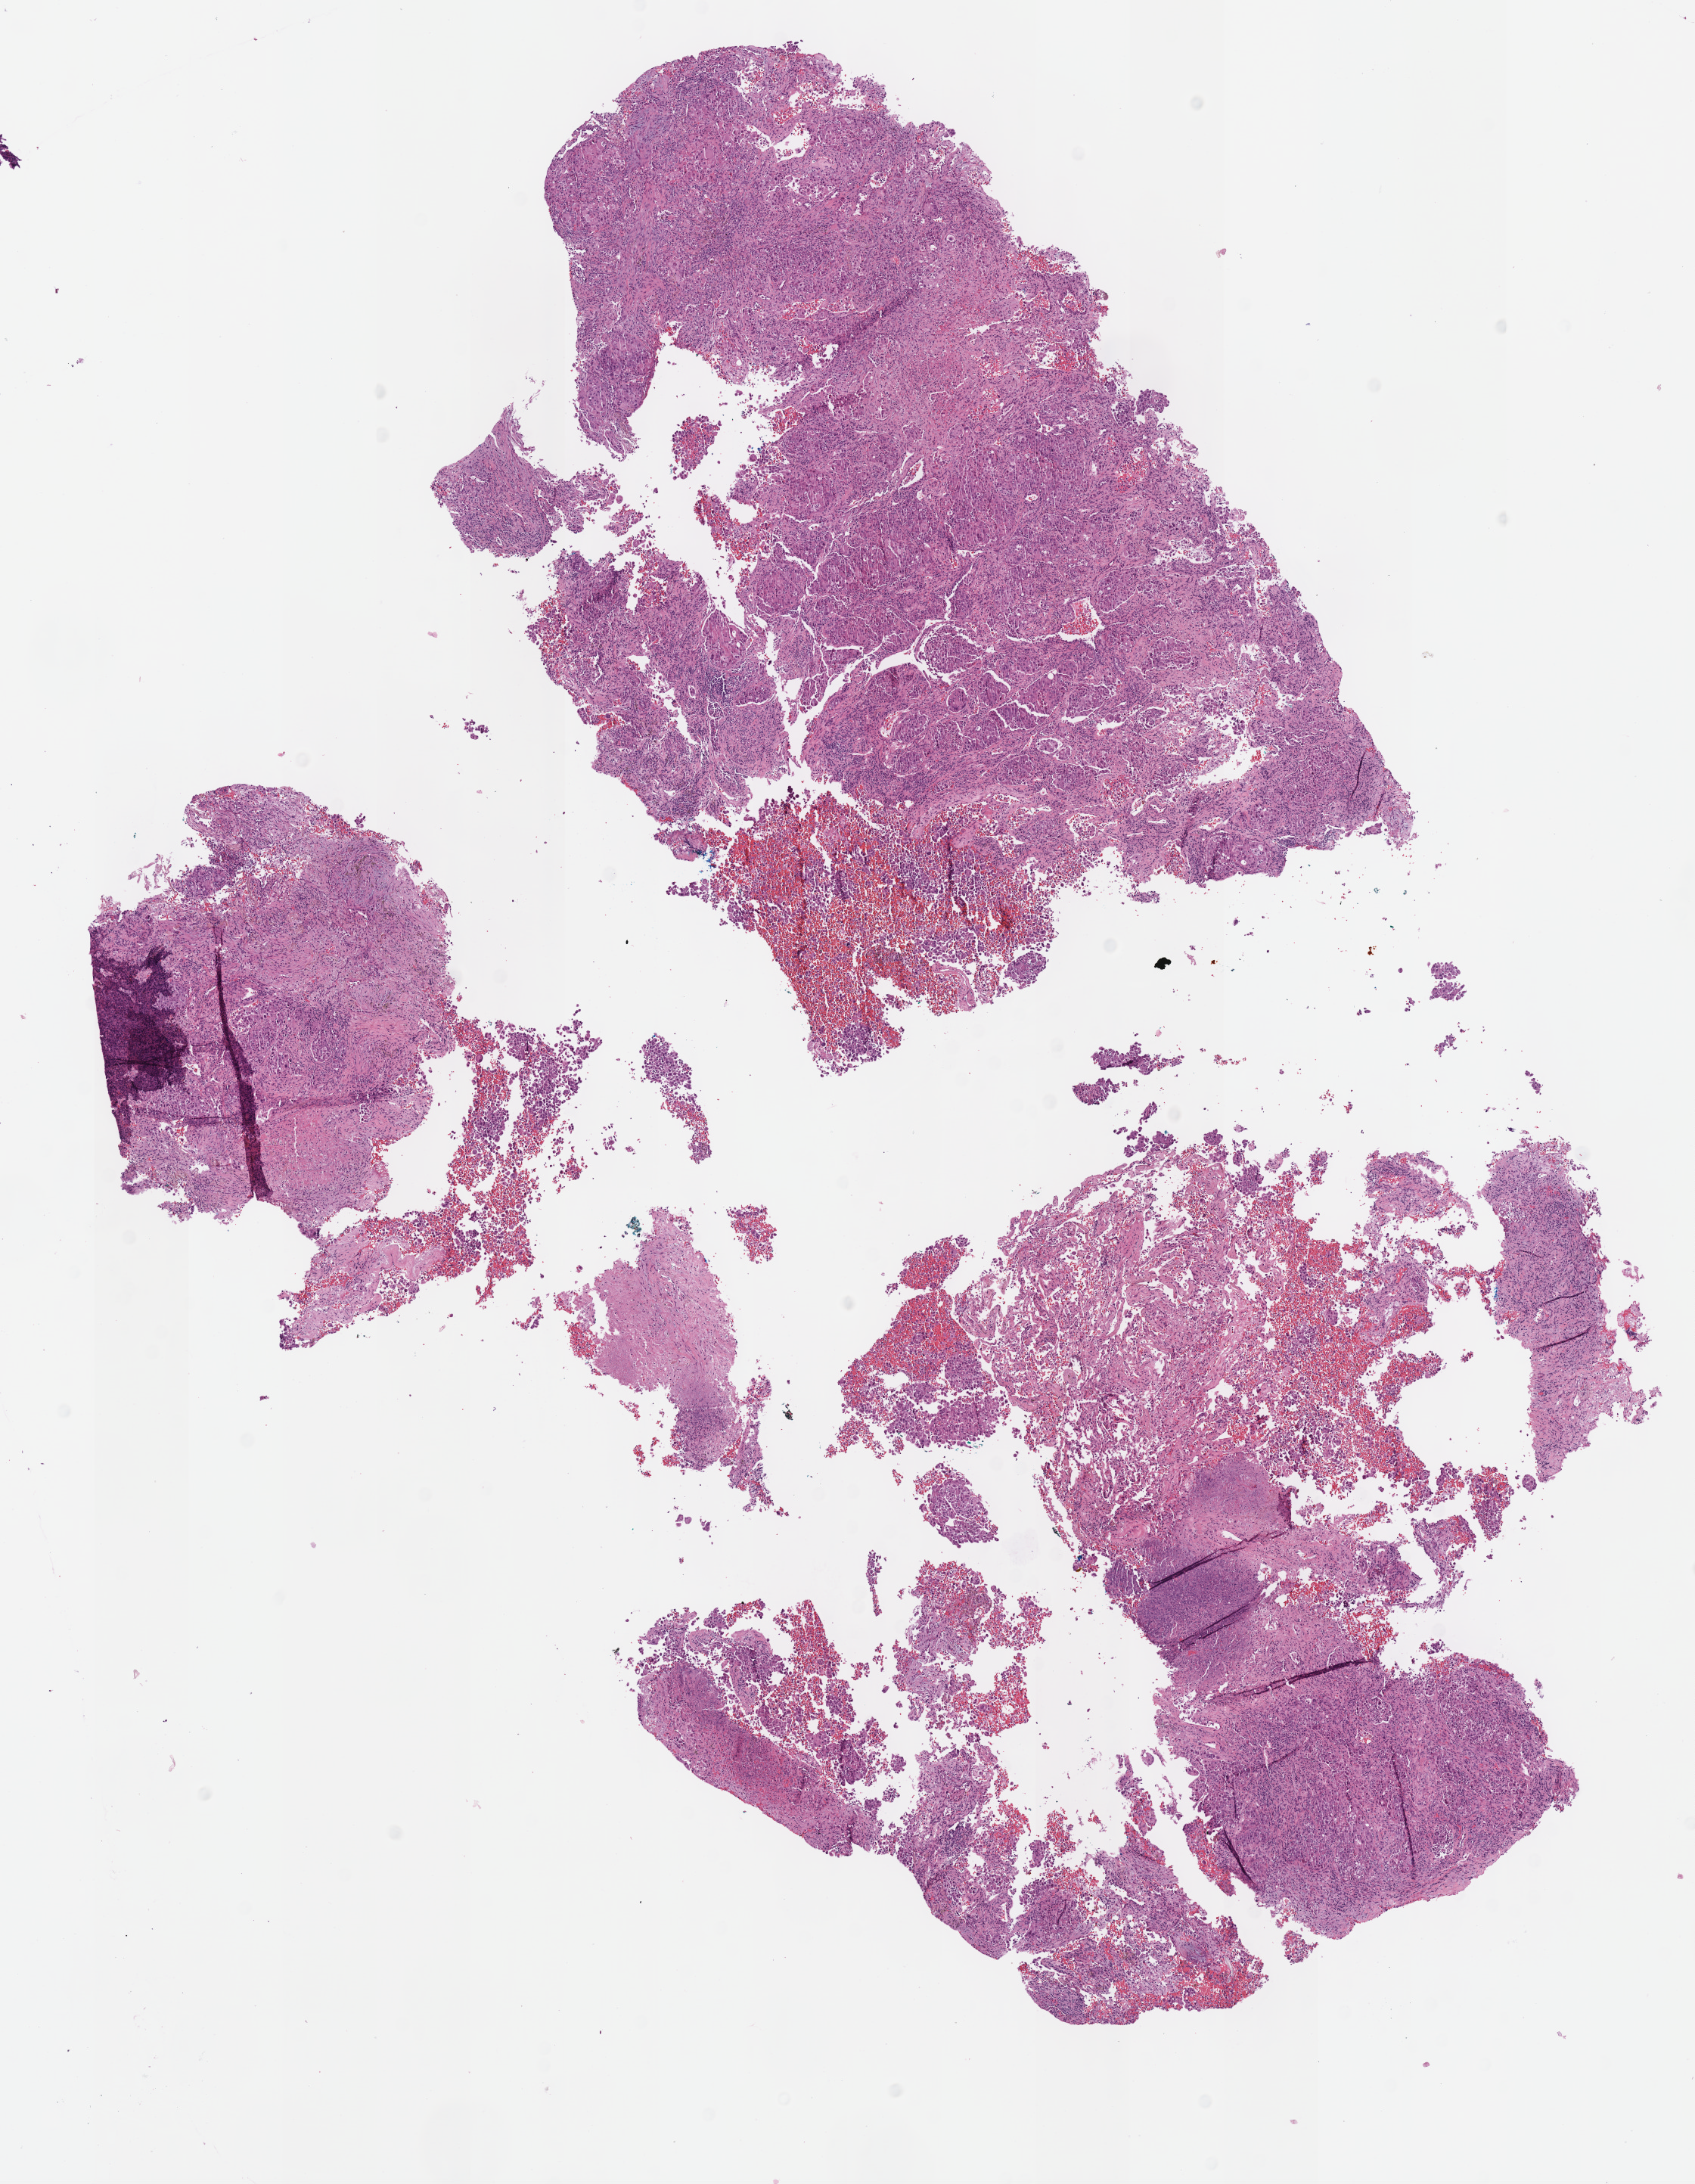
H&E-stained whole-slide image, low-resolution overview of the scanned area, about 8.8 x 11.3 mm (from a 40x scan); formalin-fixed paraffin-embedded (FFPE) diagnostic section; primary tumour sample from the lung. Female patient; age at initial diagnosis 61 years.
* AJCC pathologic stage: IA
* diagnosis: Adenocarcinoma, NOS